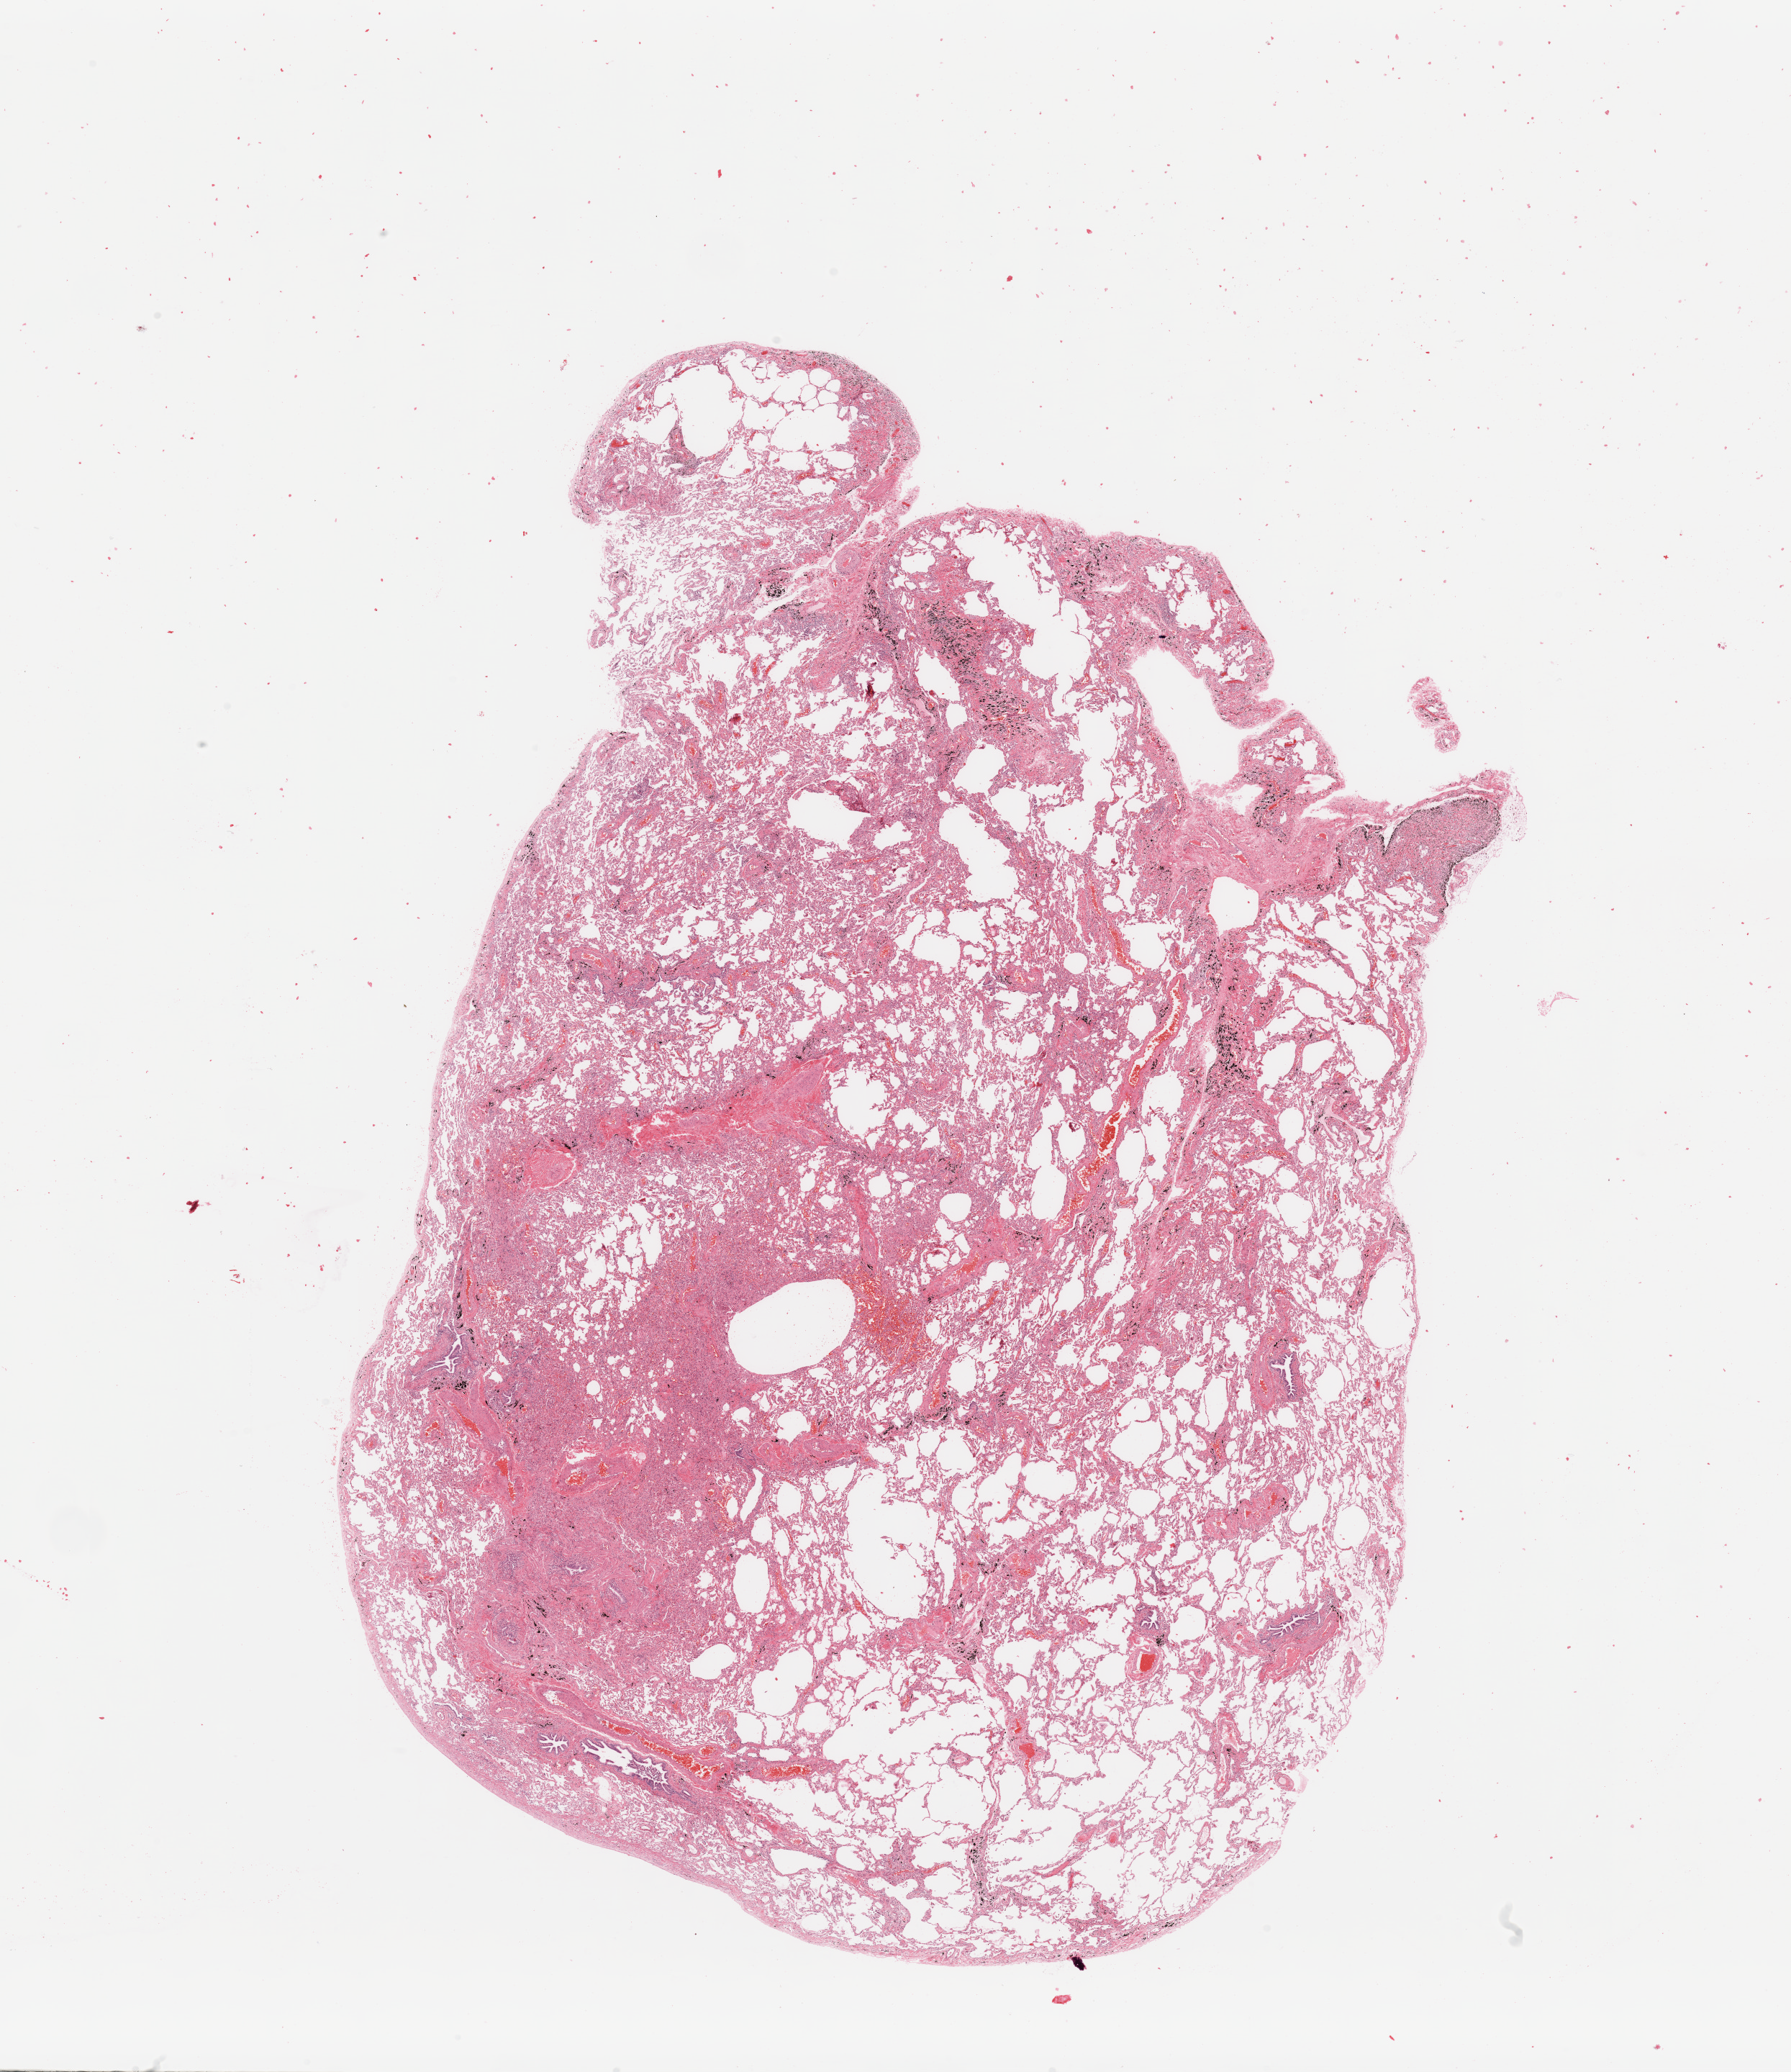
Digitized H&E tissue section (whole slide), low-resolution overview of the scanned area, about 19.7 x 22.8 mm. Normal (non-tumour) tissue sample, lung. 58-year-old male patient.
• this section: normal (non-tumour) tissue from the same patient
• patient diagnosis: Adenocarcinoma, NOS